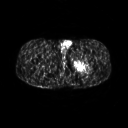
FDG PET of an extremity soft-tissue mass (from a PET/CT study), one axial slice. 128 × 128 image matrix. Male patient, age 27 years. Case-level facts recorded for this patient, not image findings: histological type: extraskeletal osteosarcoma; grade: high; site of the primary tumour: left adductur.
Structures marked on this image (expert contour drawn on MRI and transferred to this co-registered scan by the dataset authors):
- gross tumour volume (mass): bounding box <71,54,95,74> (left, top, right, bottom; pixels)